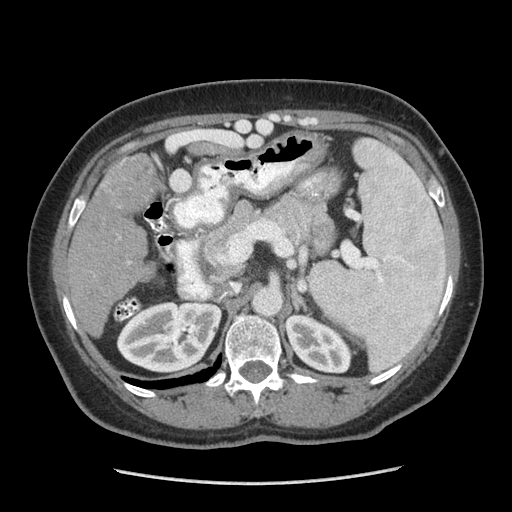
Contrast-enhanced abdominal CT (liver protocol), one axial slice. Slice 144 of 185 in the series (ordered by position). Reconstruction kernel STANDARD. Soft-tissue window (W 400 / L 40 HU). 2.5 mm slice thickness. 512 × 512 image matrix, field of view 360 × 360 mm. From the clinical record (not read from this slice): diagnosis: hepatocellular carcinoma (patient treated with transarterial chemoembolisation; whether this scan precedes or follows treatment is not stated here); TNM stage (as recorded): Stage-I; Child-Pugh class: A.
Outlined on this slice (semi-automatic segmentation, software-assisted and operator-edited):
- liver parenchyma outside the tumour (the mass and vessels are separate outlines, so this box may not span the whole liver): bounding box (x1, y1, x2, y2) in pixels: (66, 154, 162, 334)
- mass: (97, 156, 159, 212)
- liver vessels: (128, 159, 157, 263)